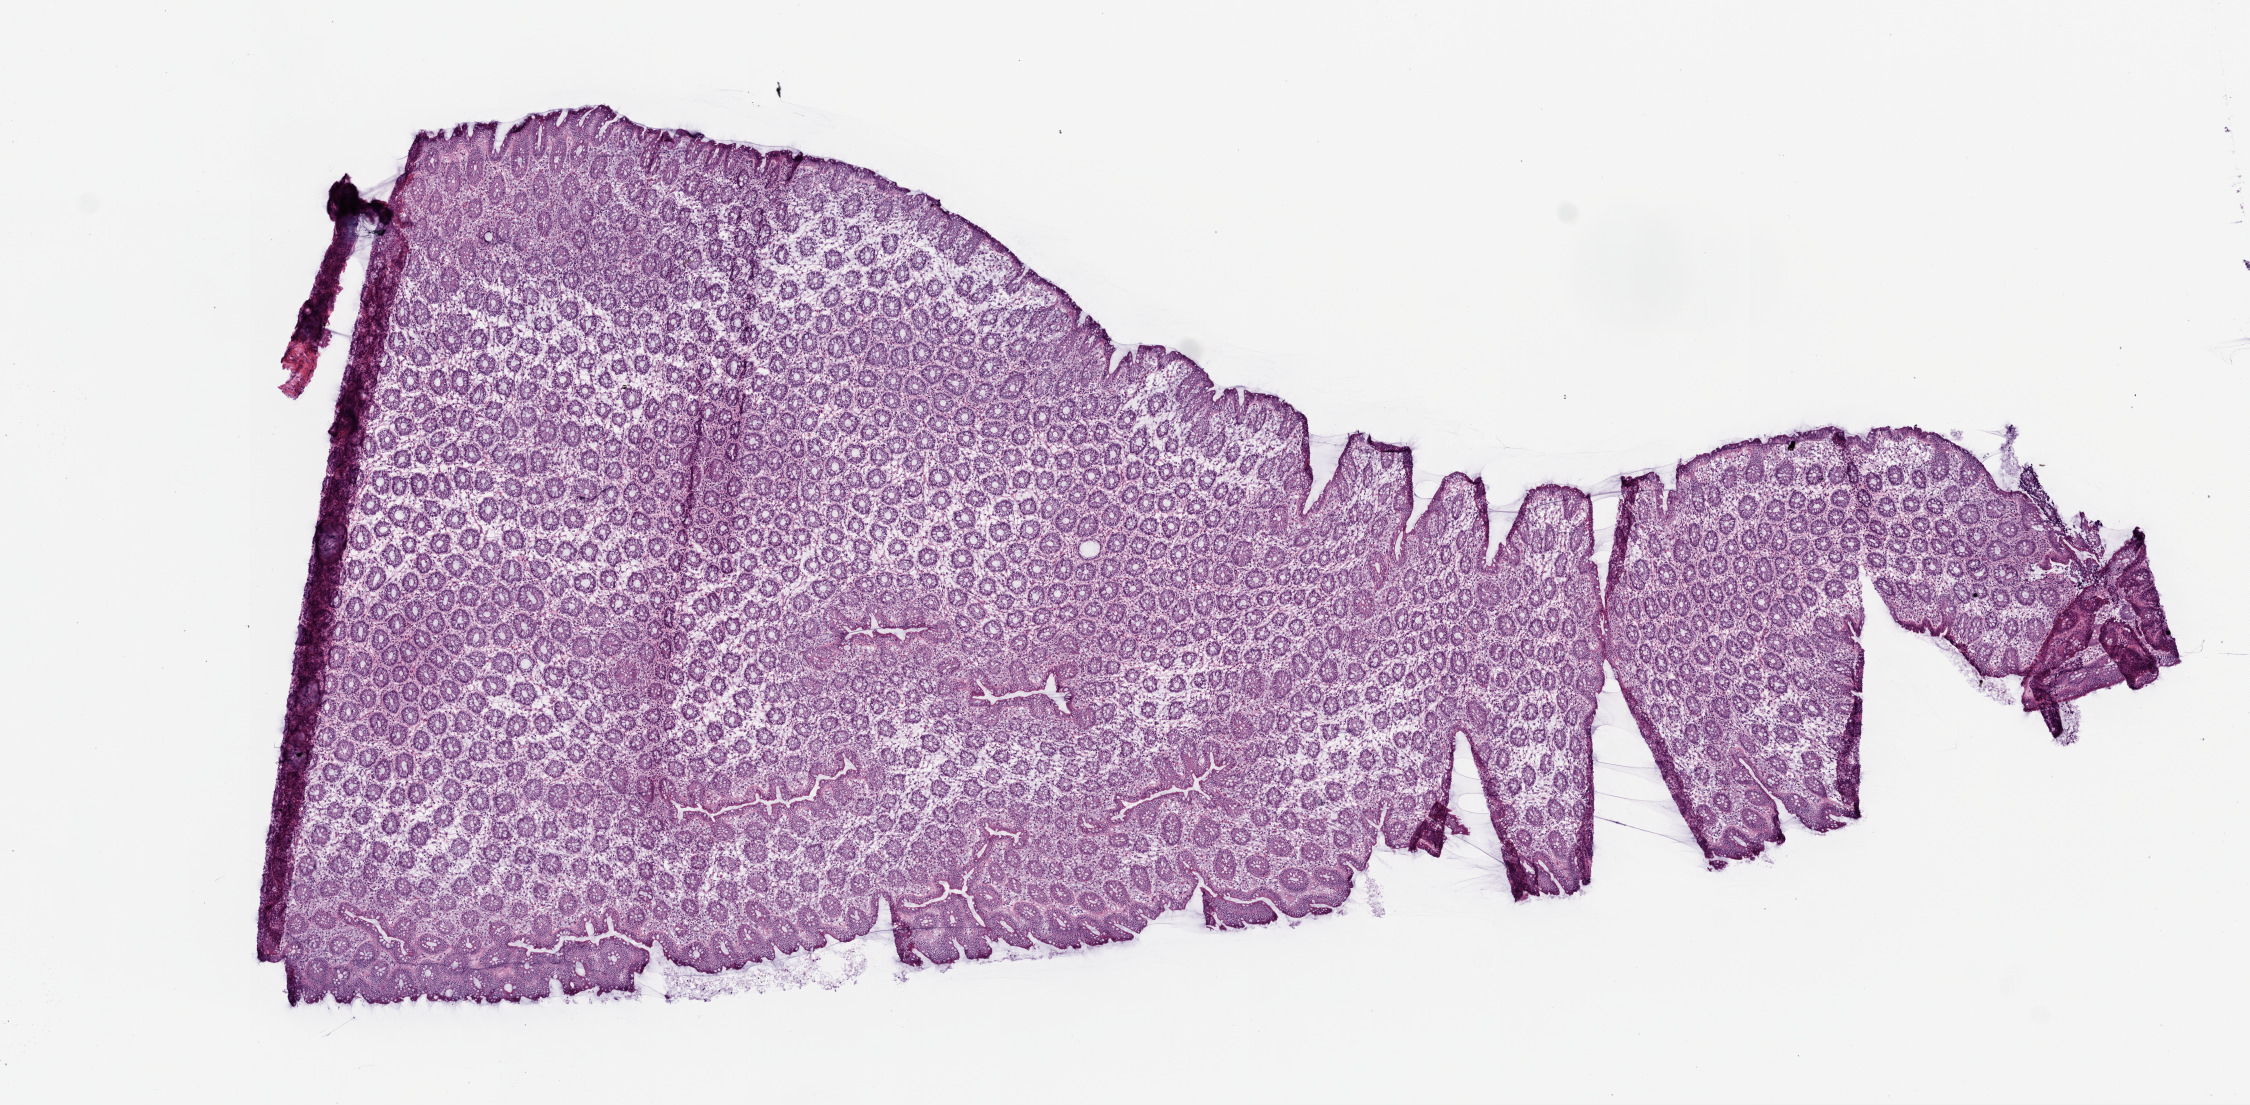
Digitized H&E-stained tissue section (whole slide) — low-resolution overview of the scanned area, about 9.0 x 4.4 mm (from a 20x scan), frozen section from the top of the tissue portion, sample: solid tissue normal (non-tumour tissue), colon. Male patient; age at initial diagnosis 67 years.
This section: solid tissue normal sample (biorepository sample class). Patient diagnosis: Adenocarcinoma, NOS (ascending colon).